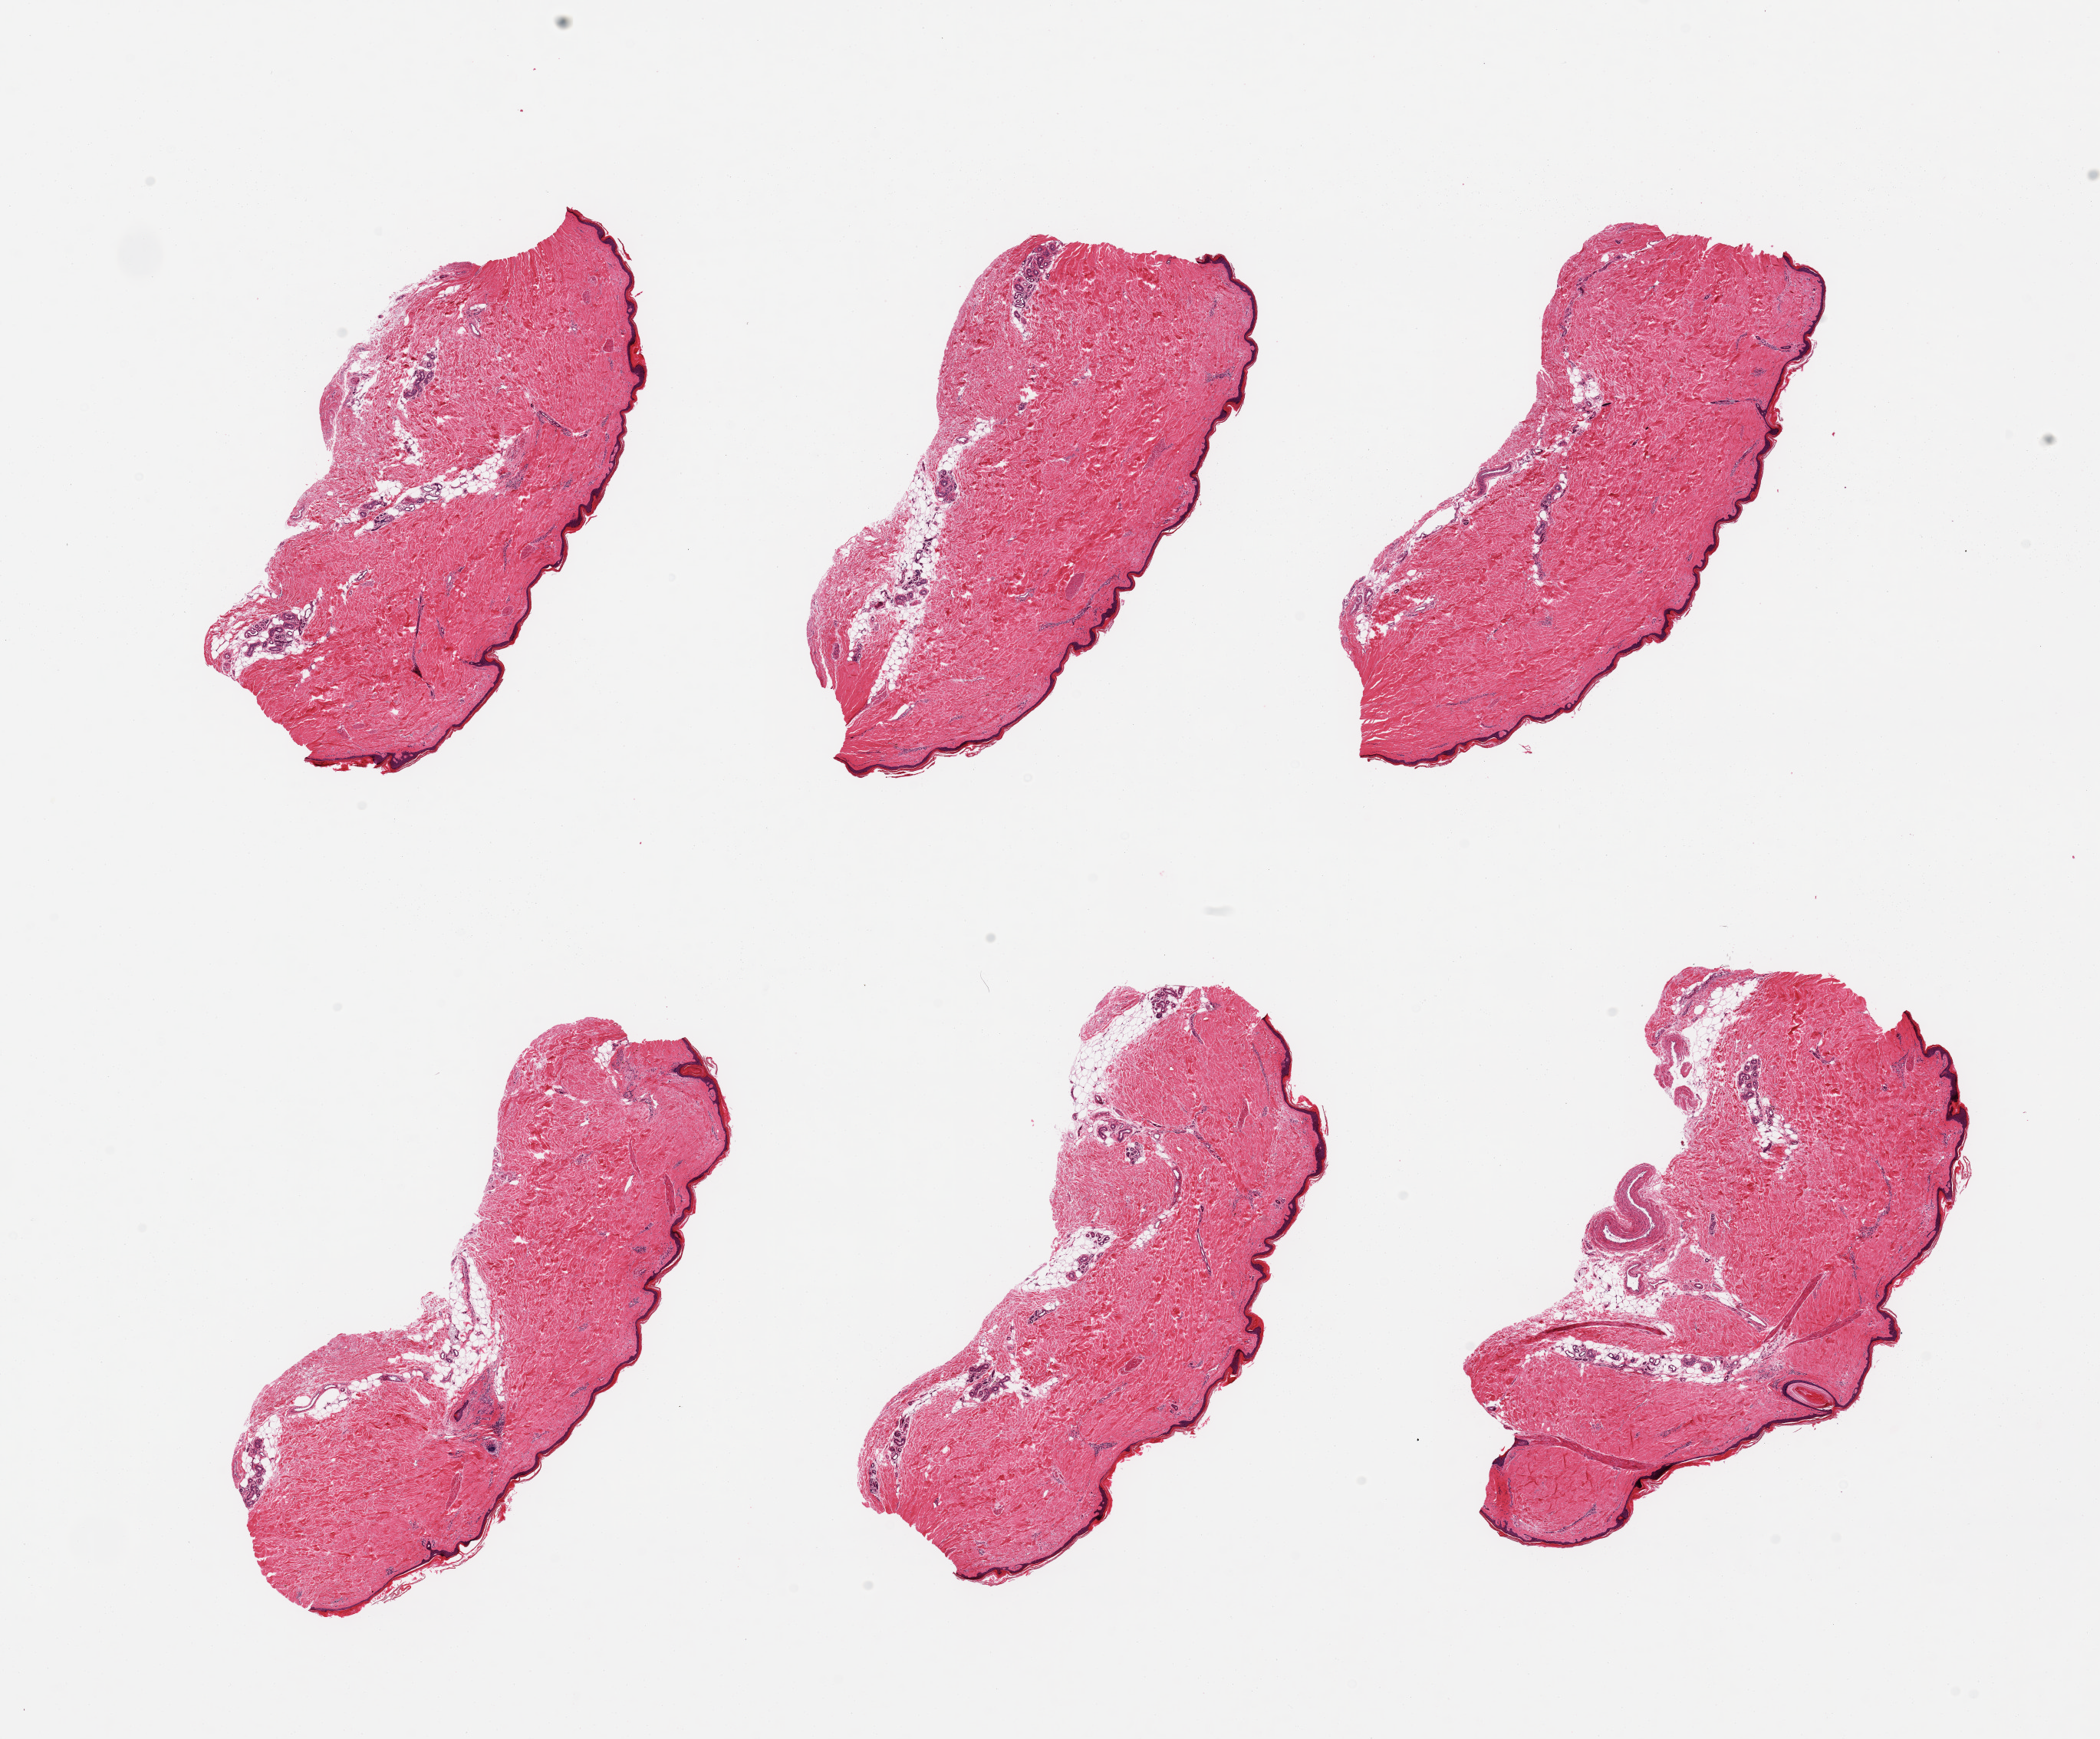
Digitized hematoxylin and eosin (H&E)-stained section, shown as a low-resolution overview of the whole scanned area (about 21.7 x 17.9 mm), PAXgene-fixed paraffin-embedded (PFPE) section, target tissue: skin of lower leg, donor tissue sample. Donor sex: male.
* review note (as recorded): 6 pieces, trace dermal fat; squamous epithelium is ~30-40 microns